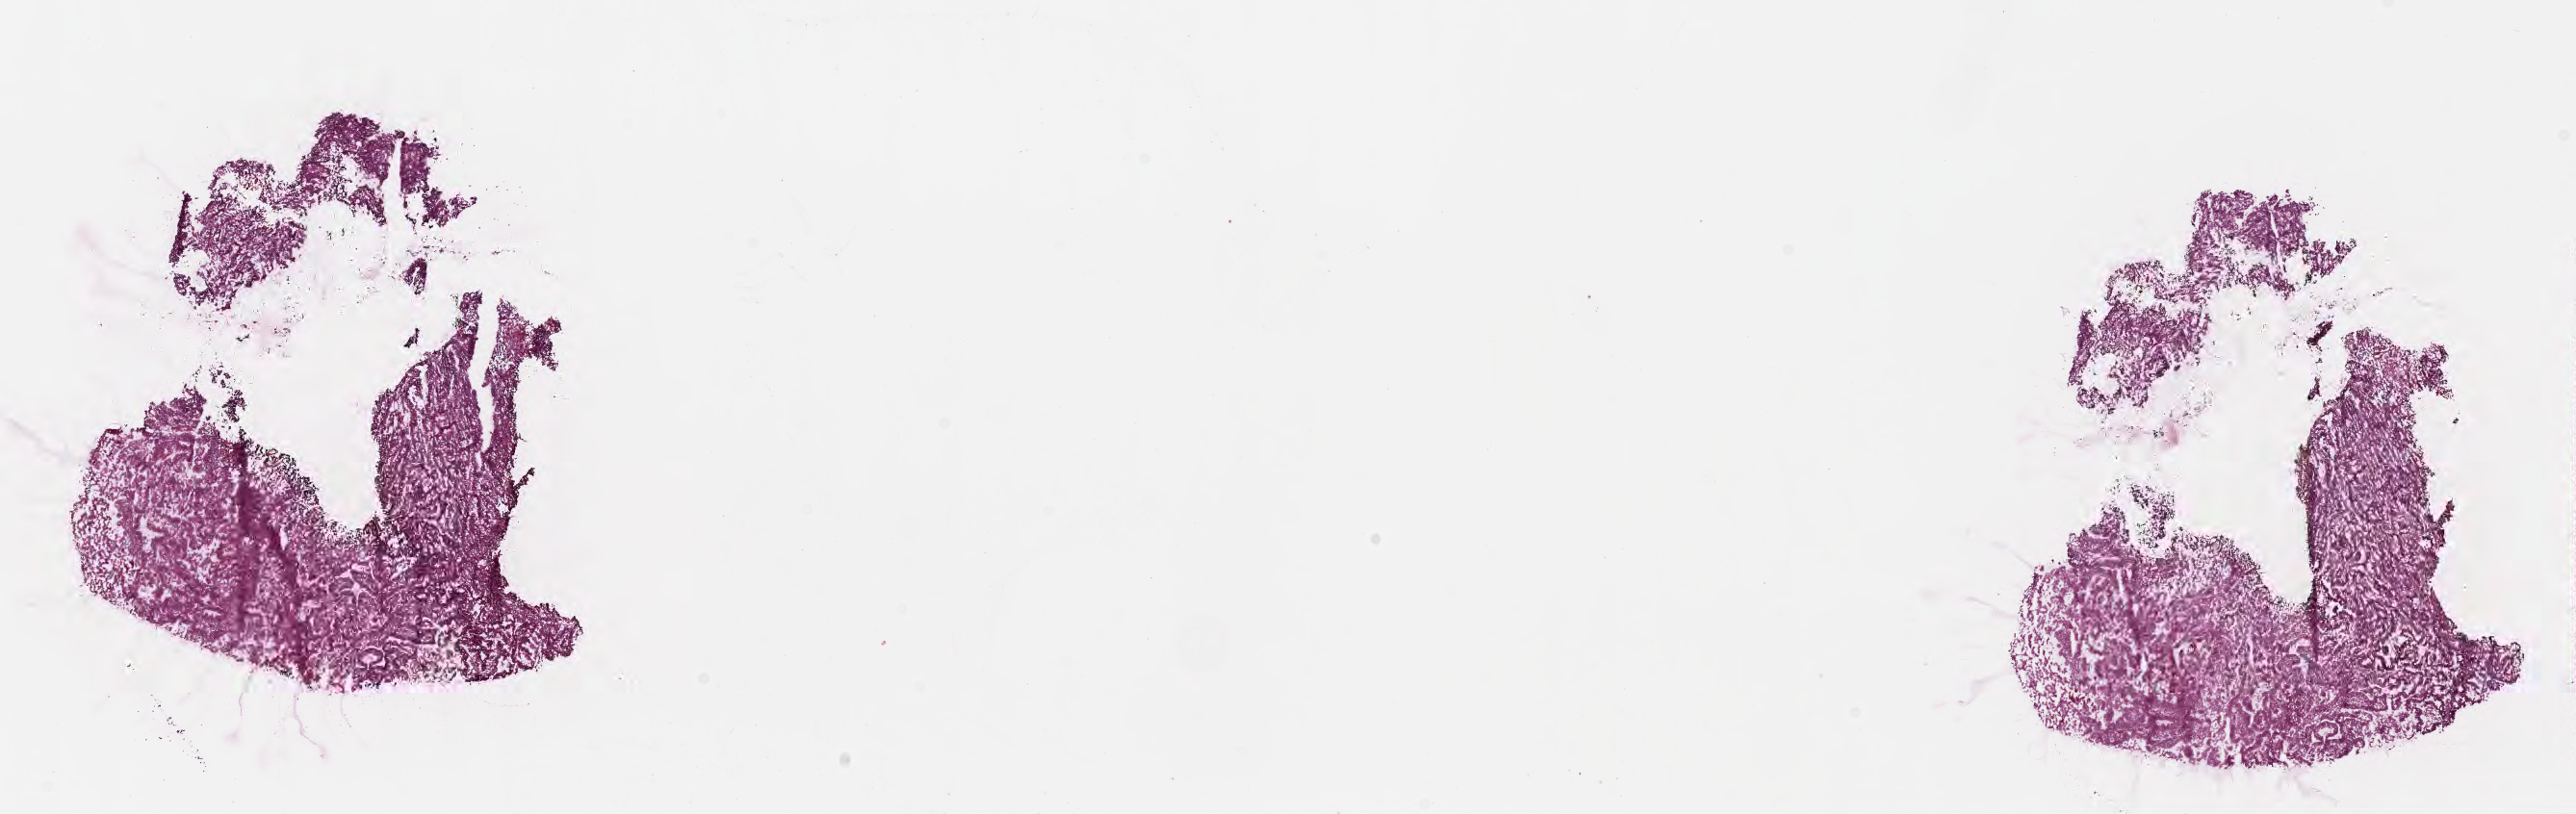
Digitized hematoxylin and eosin (H&E)-stained section, low-resolution overview of the scanned area, about 21.6 x 6.8 mm; frozen section; specimen: premalignant lesion from a patient with noninfiltrating intraductal papillary adenocarcinoma; site: gallbladder. Male patient; age at initial diagnosis 65 years.
This section: sample classed premalignant; the patient's recorded diagnosis is given above.